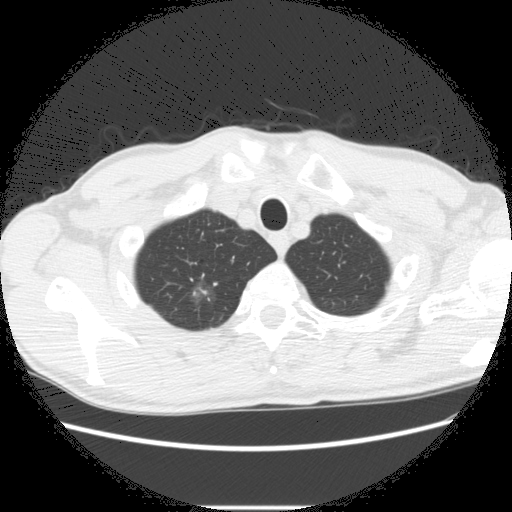
Low-dose screening chest CT, one axial slice. Slice 254 of 282 in the series (ordered by position). Reconstruction kernel STANDARD. Lung window (W 1500 / L -600 HU). 2.5 mm slice thickness. 512 × 512 image matrix.
Structures marked on this image (outlined manually by an expert reader):
- lesion 2 (nodule, upper lobe of right lung): bounding box [x1, y1, x2, y2] px = [192, 283, 211, 304]